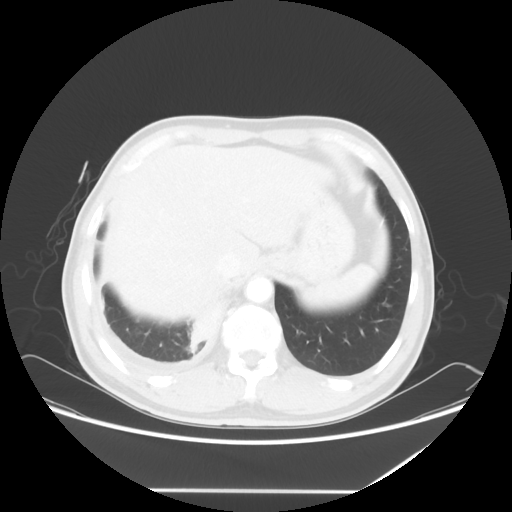
Chest CT, one axial slice. Slice 10 of 60 in the series (ordered by position). Lung window (W 1500 / L -600 HU). 5 mm slice thickness. 512 × 512 image matrix, field of view 419 × 419 mm. Male patient, age 48 years. Case-level facts recorded for this patient, not image findings: clinical TNM (as recorded): T3 N3 M1a.
Outlined on this slice (bounding box drawn by a radiologist):
- lung tumour (recorded histology: squamous cell carcinoma): bounding box [x1, y1, x2, y2] px = [189, 294, 229, 357]